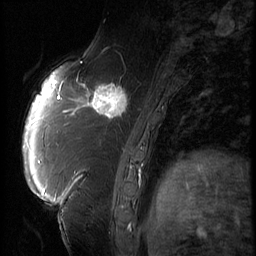
Breast MRI (dynamic contrast-enhanced), one sagittal slice; position 22 of 66 along the scan axis; 3 images stored at this slice position (order not interpretable as contrast timing); 1.5 T; TE 4.2 ms, TR 9 ms; 2.5 mm slice thickness; 256 × 256 image matrix, field of view 180 × 180 mm. Female patient, age 57 years. From the clinical record (not read from this slice): setting: breast cancer imaged before/during neoadjuvant chemotherapy; receptor status: triple-negative.
Structures marked on this image (semi-automatic segmentation, software-assisted and operator-edited):
- analysis volume of interest (the breast-tissue region the enhancement analysis was run in; not a lesion): bounding box <86,74,138,129> (left, top, right, bottom; pixels)
- tumour enhancement mask (voxels above the 140 % enhancement threshold inside the analysis volume of interest): <86,81,130,122>